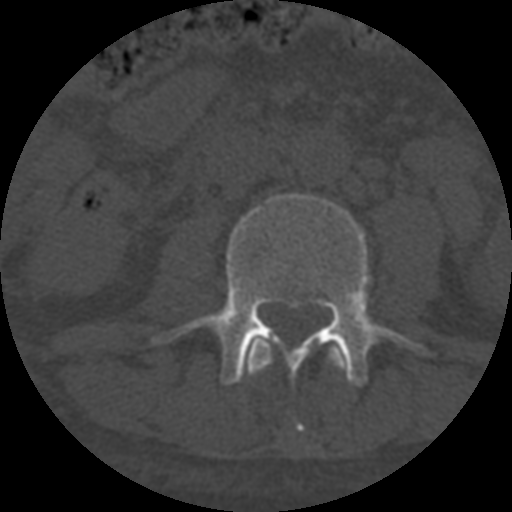
CT including the spine, one axial slice. Position 240 of 708 along the scan axis. Reconstruction kernel STANDARD. One of 3 acquisitions stored at this slice position. Bone window (W 1800 / L 400 HU). 1.25 mm slice thickness. 512 × 512 image matrix, field of view 160 × 160 mm. Patient age 55 years. From the clinical record (not read from this slice): primary cancer: colon; vertebrae with lytic lesions (as recorded): T12, L1, L5.
Annotated regions visible in this slice (semi-automatically segmented with operator editing):
- L2 vertebra: bounding box [x1, y1, x2, y2] px = [246, 339, 344, 376]
- L3 vertebra: [154, 193, 433, 387]